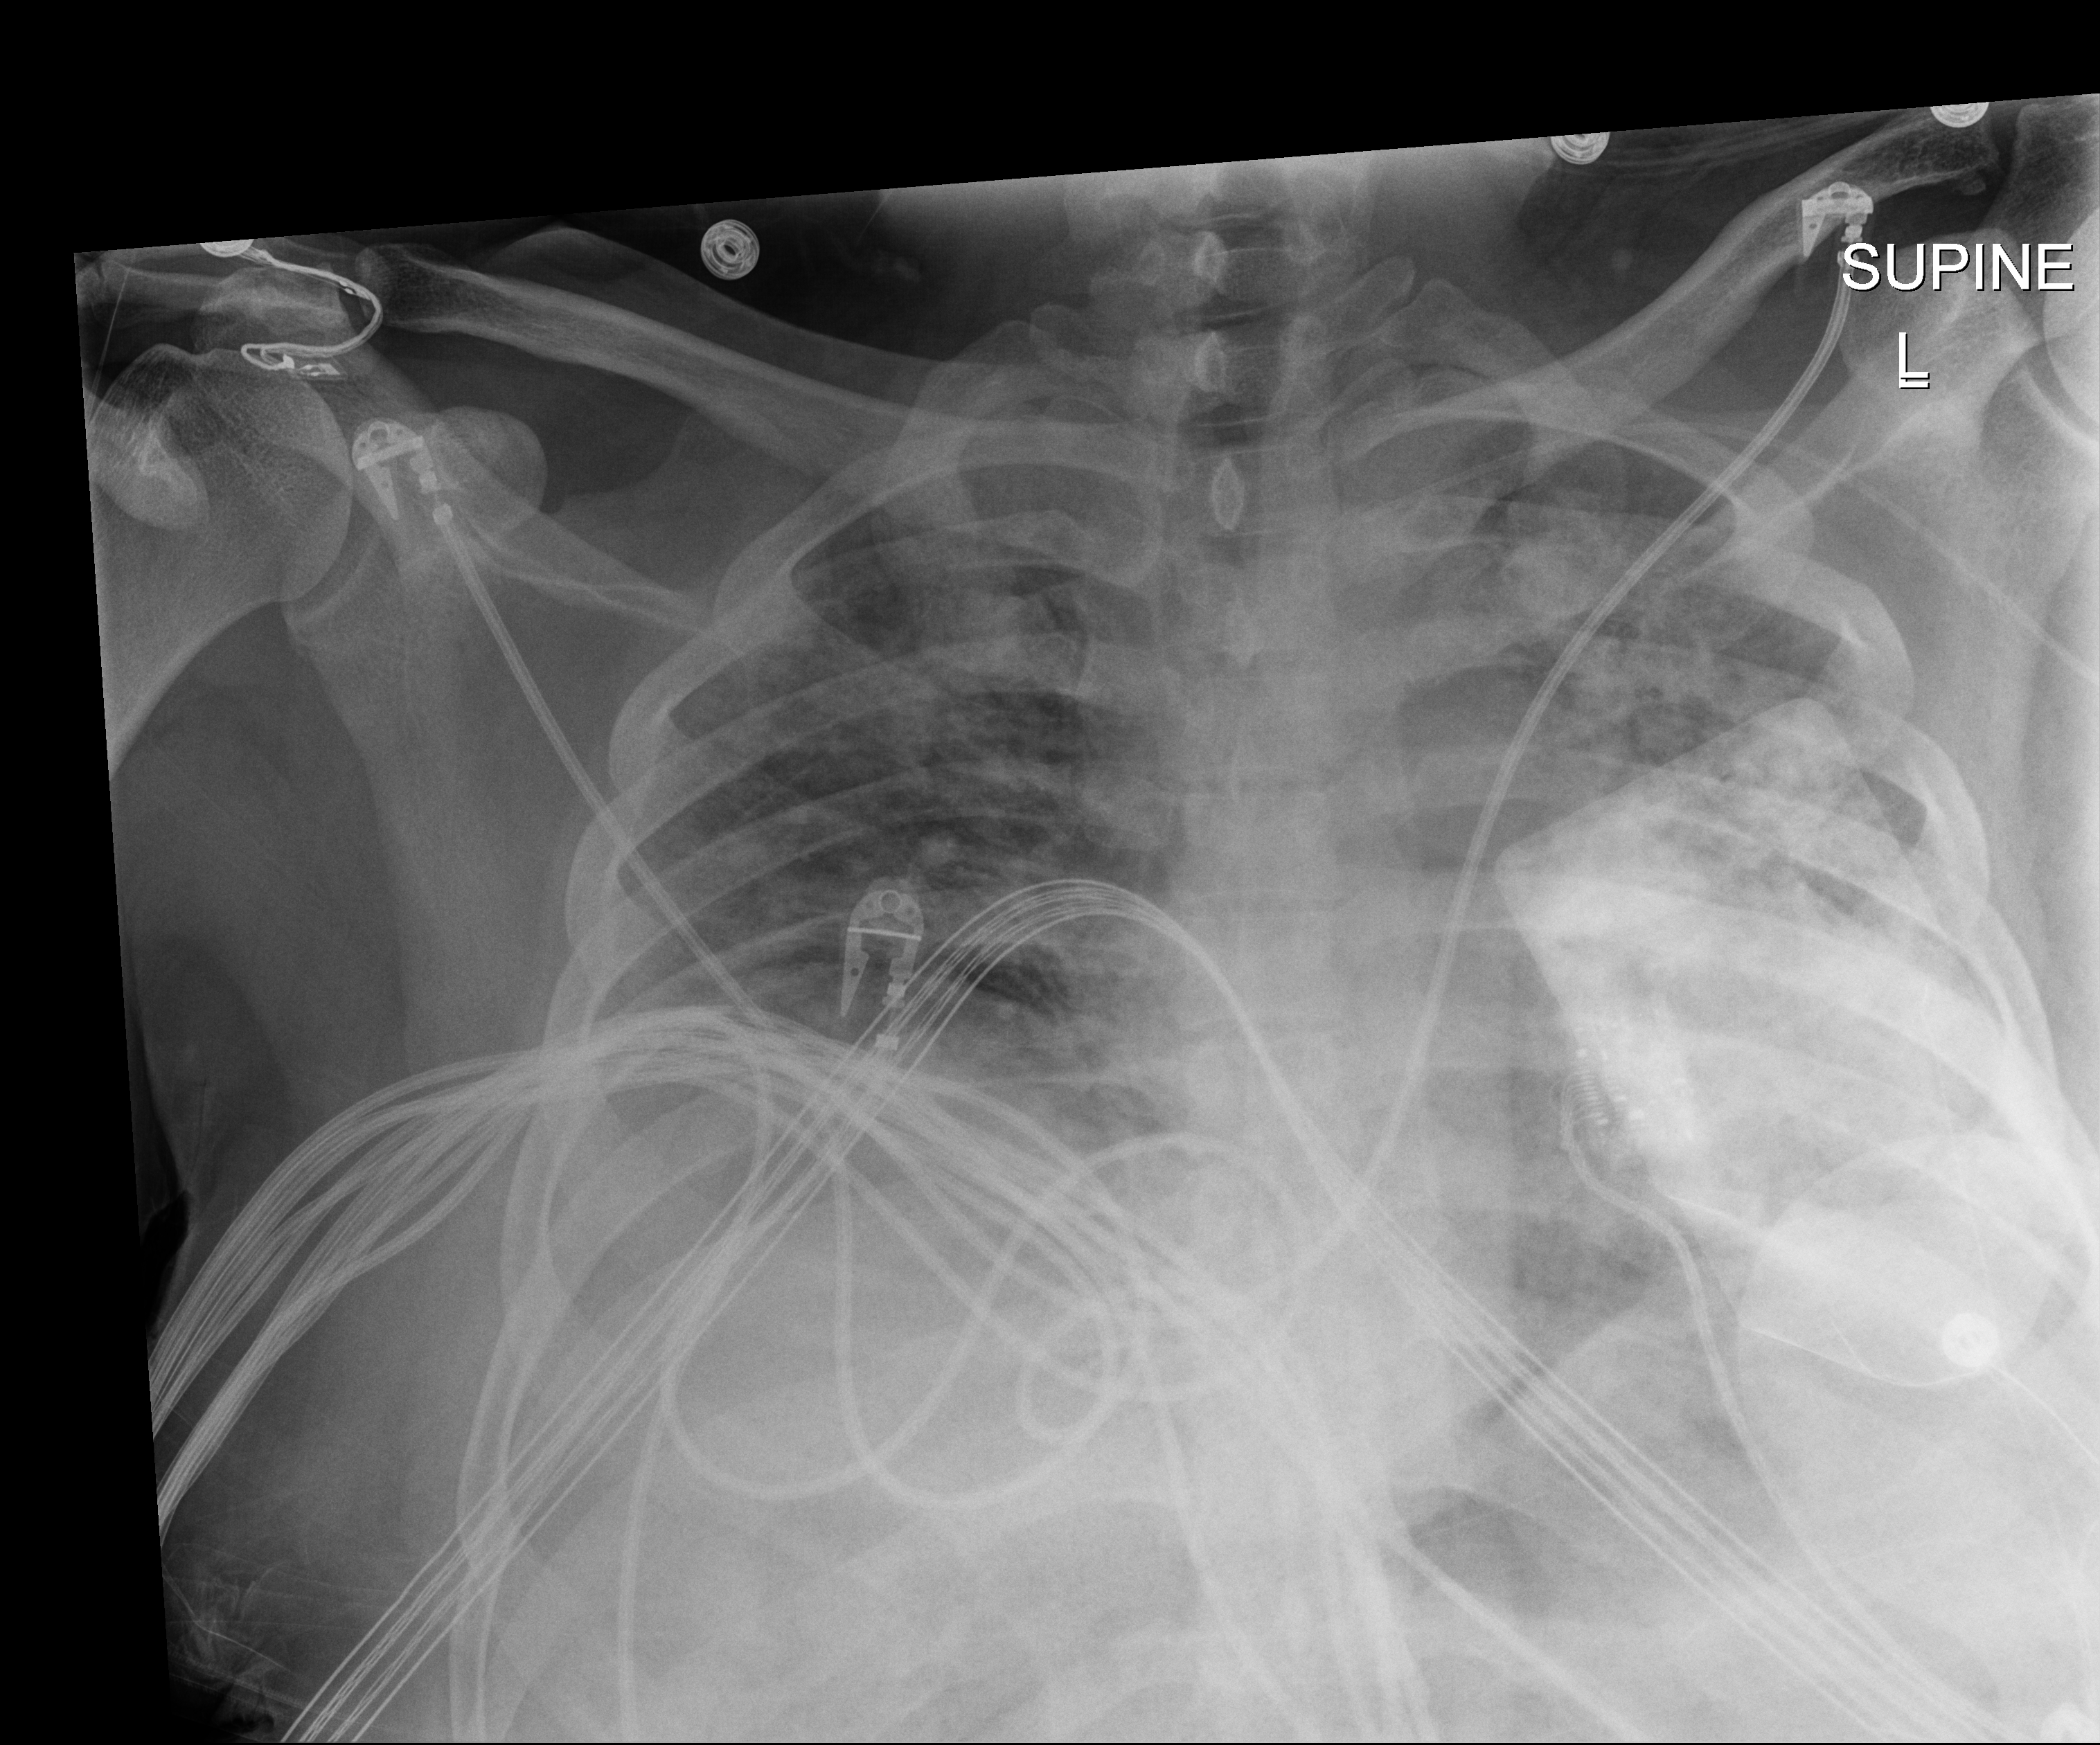
Portable chest radiograph, anteroposterior (AP) projection. Patient hospitalised with COVID-19; male, aged 18–59 years.
From the hospital-stay record, not from the radiograph (when in the stay this image was taken is not recorded):
- admitted to intensive care during this hospital stay: yes